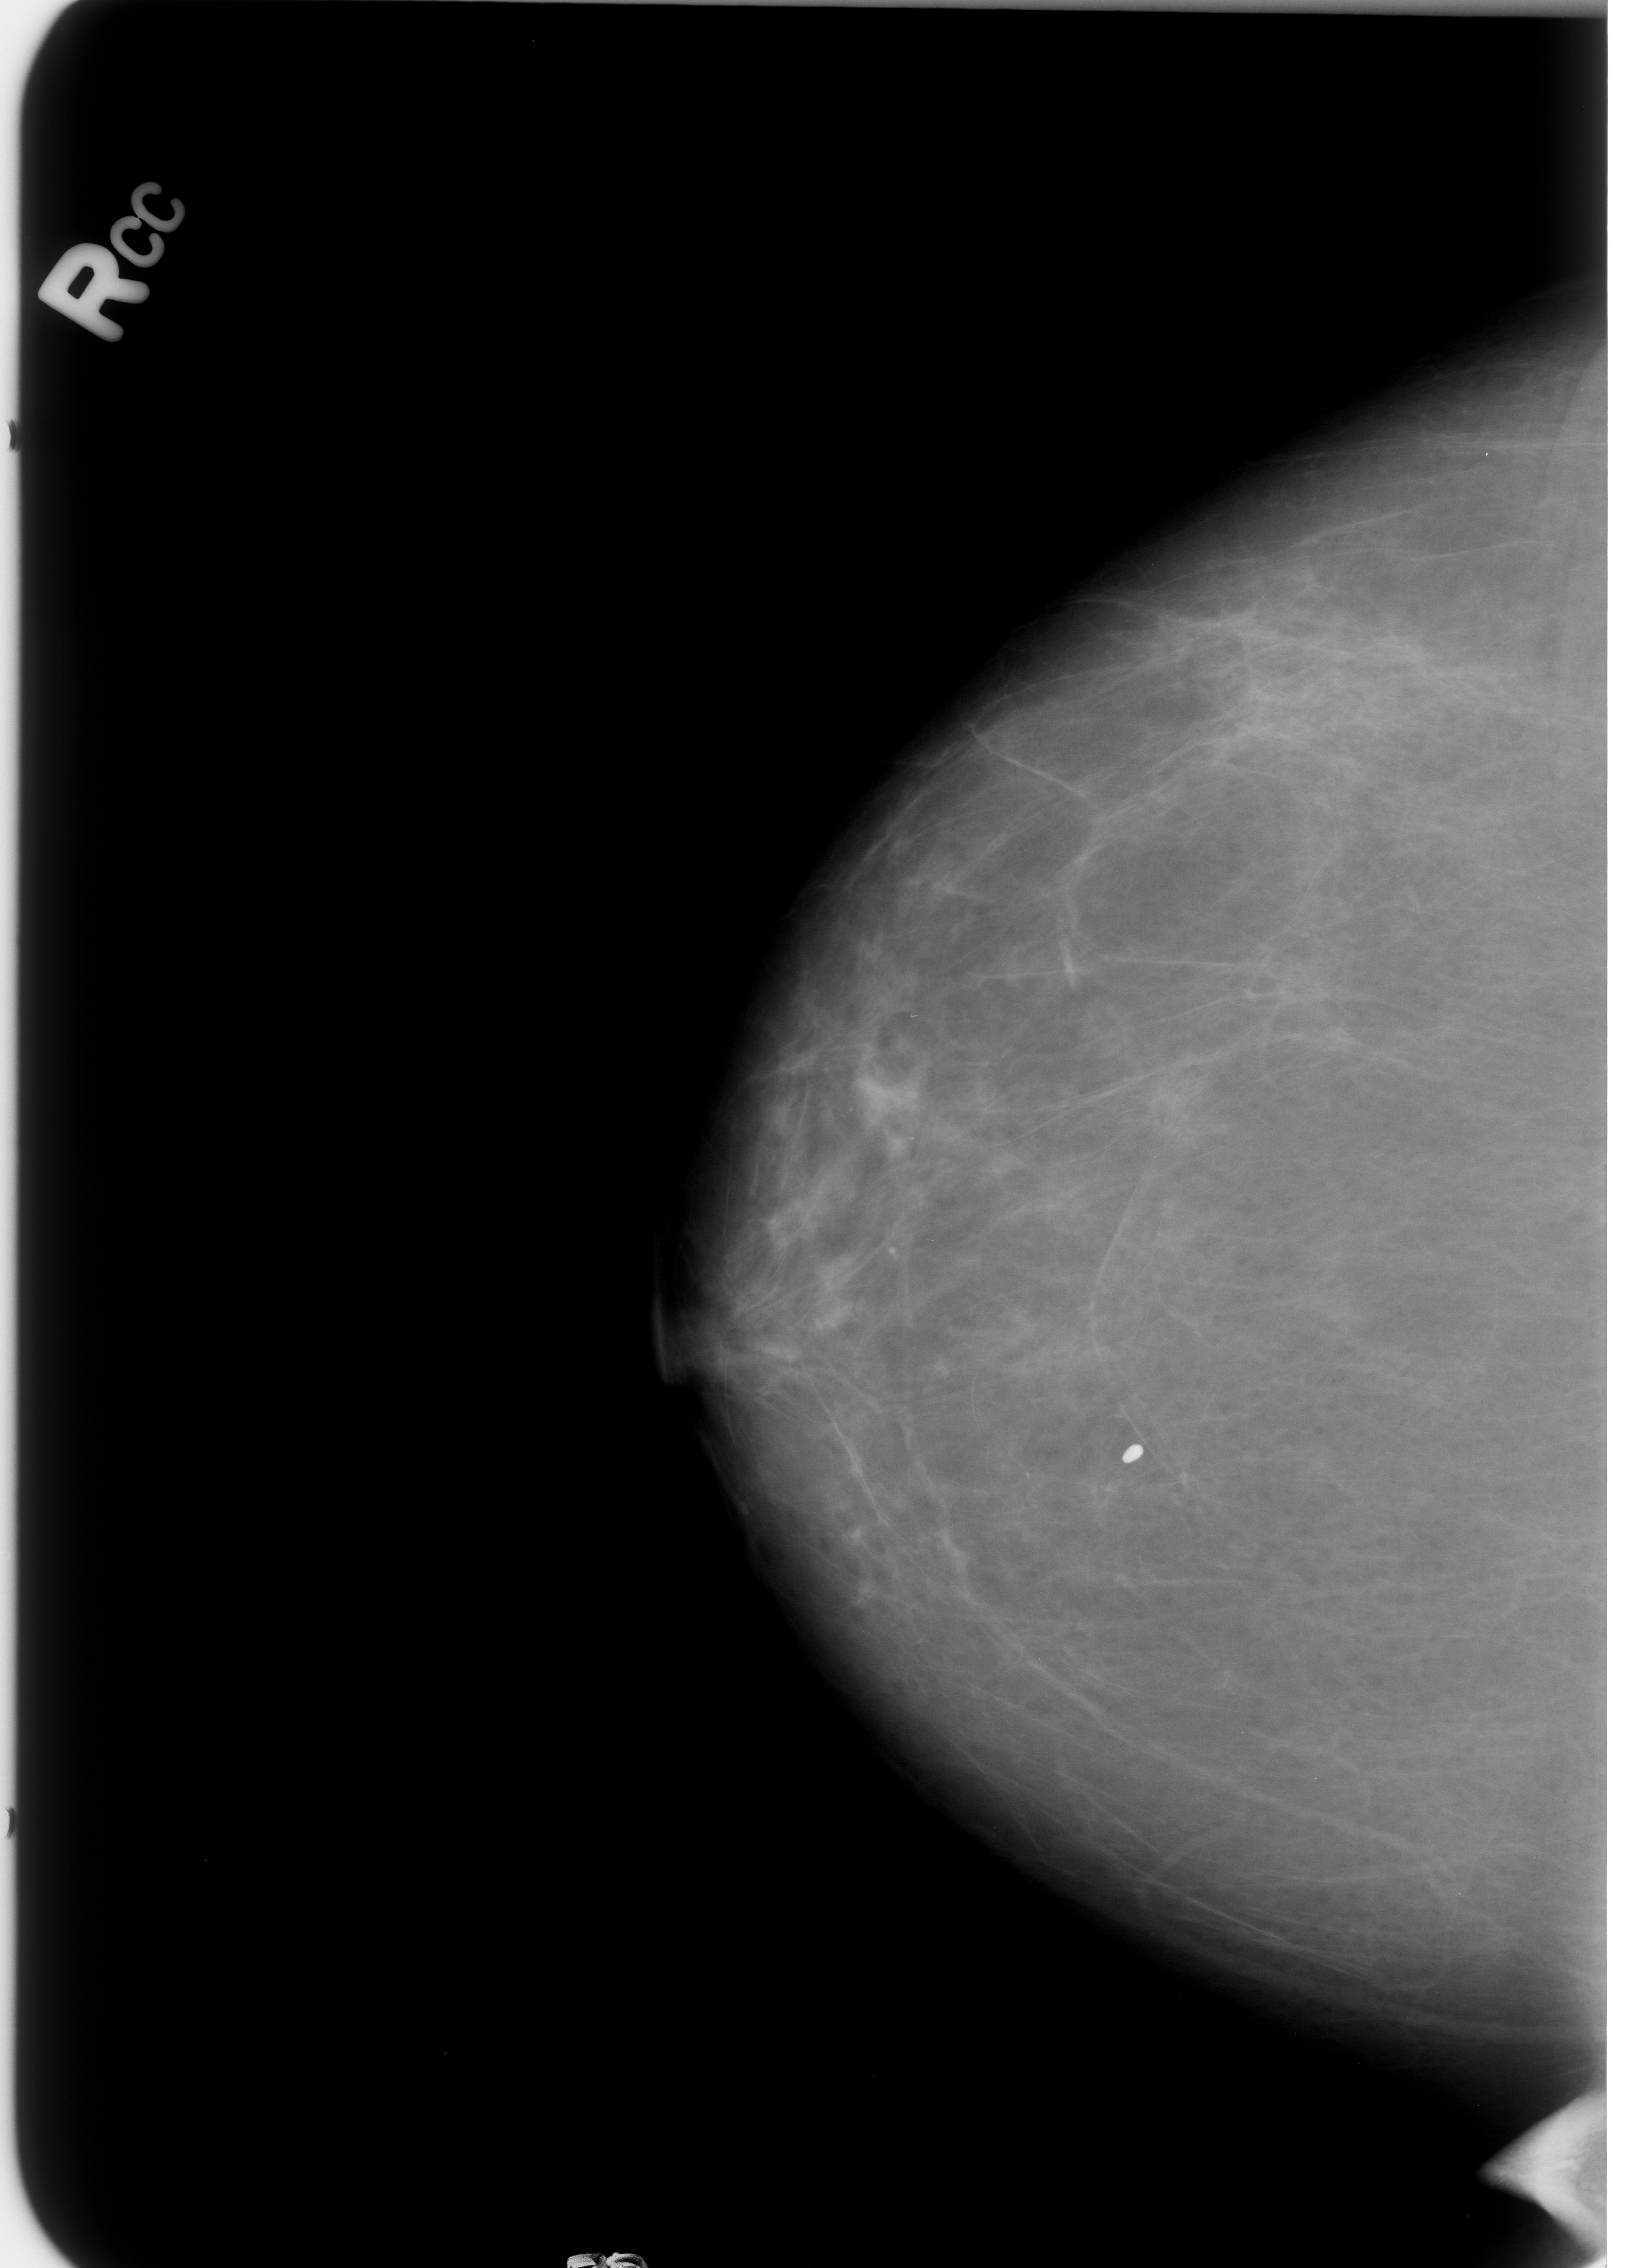
Scanned film-screen mammogram. Right breast. CC view. BI-RADS breast density category 1 (scale 1–4). 1628 × 2268 image matrix.
Expert-marked regions of interest on this film, with their recorded descriptors:
- calcifications, morphology coarse; BI-RADS assessment category 2; subtlety rating 5 on a 1 (subtle) to 5 (obvious) scale; outcome (as recorded, no biopsy): benign without callback (not worked up further): bounding box (x1, y1, x2, y2) in pixels: (1115, 1430, 1154, 1476)